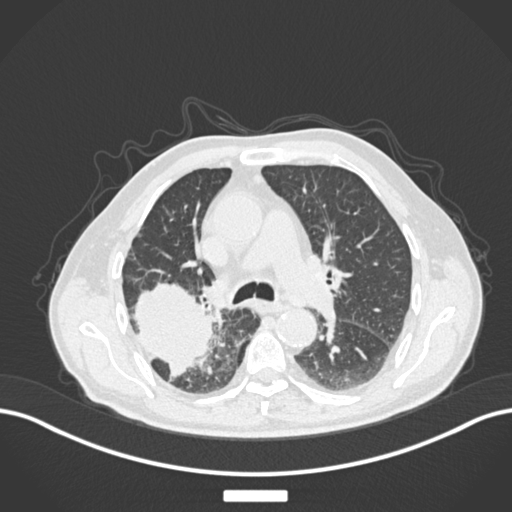
Chest CT, one axial slice; position 110 of 201 along the scan axis; reconstruction kernel B30f; 120 kVp; lung window (W 1500 / L -600 HU); 1 mm slice thickness; 512 × 512 image matrix, field of view 400 × 400 mm. Male patient, age 72 years. Case-level facts recorded for this patient, not image findings: clinical TNM (as recorded): T3 N2 M0.
Annotated regions visible in this slice (rectangle marked by the reading radiologist):
- lung tumour (recorded histology: adenocarcinoma): box from (x=131, y=273) to (x=219, y=383) px